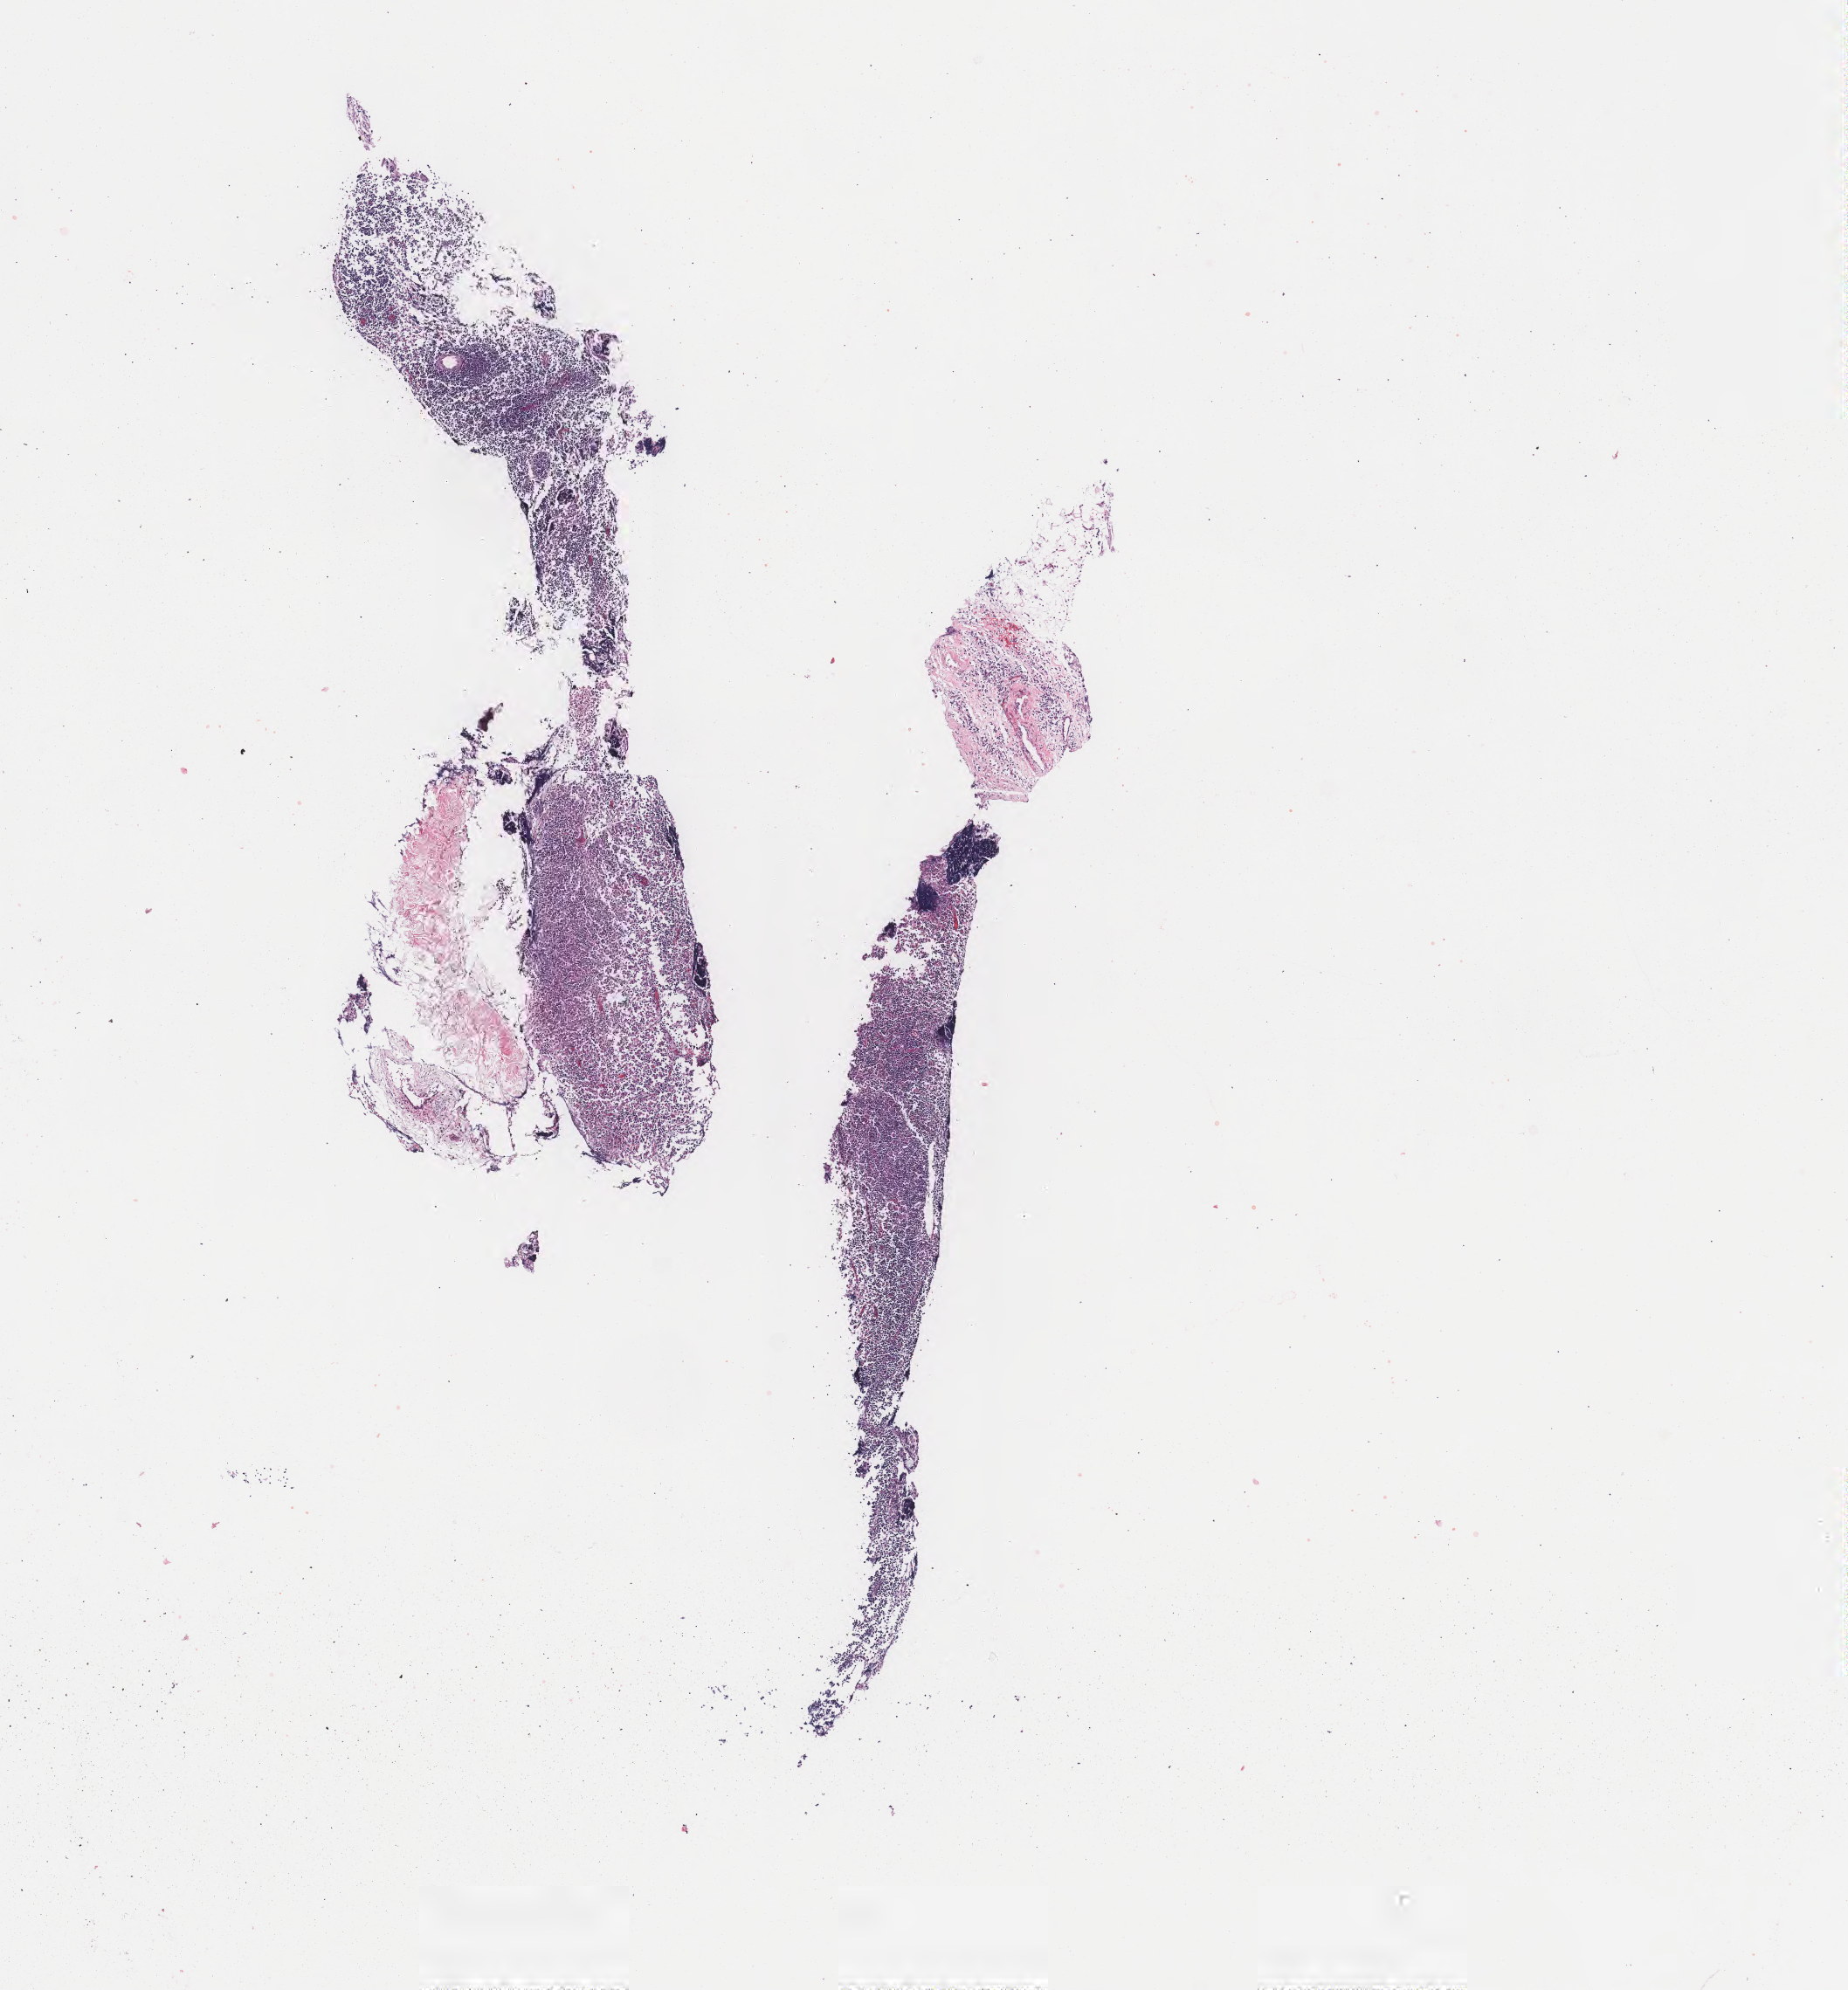
Whole-slide image, haematoxylin and eosin stain — low-resolution overview of the scanned area, about 8.4 x 9.0 mm. Formalin-fixed, paraffin-embedded (FFPE) tissue. Specimen: tumor tissue. Patient male; 30 years old.
Histologic diagnosis: Burkitt lymphoma, NOS.